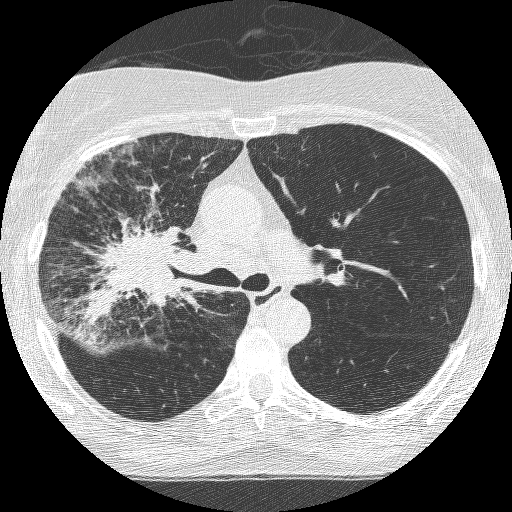
Low-dose screening chest CT, axial slice. Third screening round (two years after baseline). Lung window (W 1500 / L -600 HU). Lung (sharp) reconstruction kernel (BONE). Slice 169 of 253 in the series. Female, age 64 years at enrolment. Former smoker at enrolment.
Expert reader's lesion annotation, box from (x=85, y=213) to (x=205, y=333) px. Reader record for this screening exam (exam-level; its link to the box is not recorded): non-calcified nodule or mass ≥4 mm, right upper lobe, 49 × 43 mm, spiculated (stellate) margins, soft tissue attenuation, pre-existing on the prior screen: yes; interval growth: yes. Later outcome: lung cancer diagnosed 7 days after this screen — adenocarcinoma, NOS, right upper lobe, right middle lobe, right hilum, stage IV (AJCC 6th edition), 85 mm at pathology.